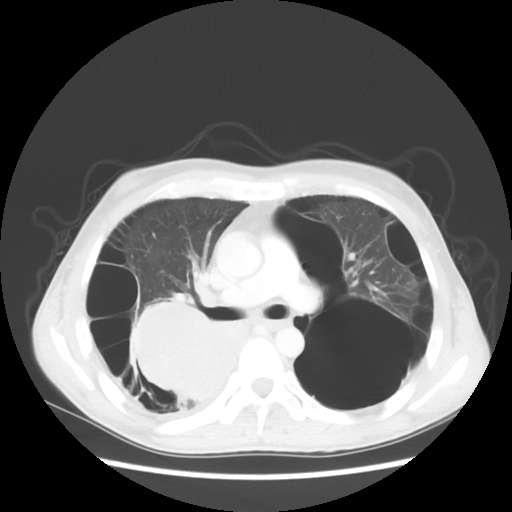
Chest CT, one axial slice. Slice 33 of 56 in the series (ordered by position). Reconstruction kernel STANDARD. 140 kVp. Lung window (W 1500 / L -600 HU). 5 mm slice thickness. 512 × 512 image matrix, field of view 351 × 351 mm. Male patient, age 41 years. From the clinical record (not read from this slice): clinical TNM (as recorded): T4 N0 M1a.
Structures marked on this image (rectangle marked by the reading radiologist):
- lung tumour (recorded histology: large cell carcinoma): box from (x=125, y=301) to (x=245, y=411) px